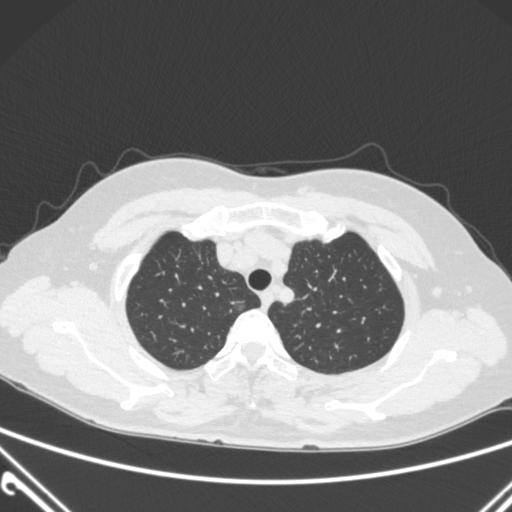
Chest CT, one axial slice. Slice 234 of 300 in the series (ordered by position). 120 kVp. Lung window (W 1500 / L -600 HU). 1 mm slice thickness. 512 × 512 image matrix, field of view 350 × 350 mm. Female patient, age 54 years. From the clinical record (not read from this slice): clinical TNM (as recorded): T1a N0 M0.
Structures marked on this image (bounding box drawn by a radiologist):
- lung tumour (recorded histology: adenocarcinoma): box from (x=230, y=298) to (x=250, y=315) px